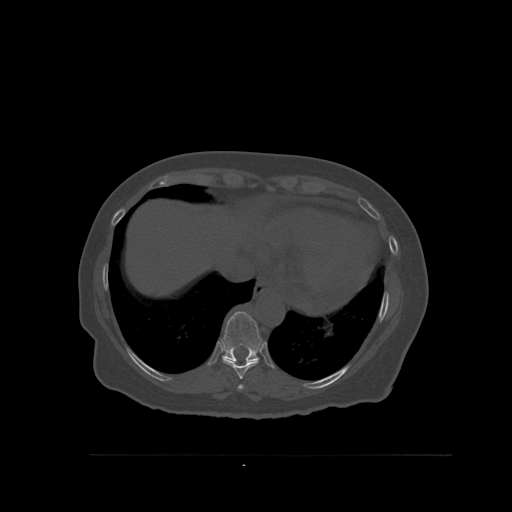
CT including the spine, one axial slice; position 328 of 527 along the scan axis; bone window (W 1800 / L 400 HU); 1.5 mm slice thickness; 512 × 512 image matrix, field of view 470 × 470 mm. Patient: female, 73 years. Case-level facts recorded for this patient, not image findings: primary cancer: breast; vertebrae with lytic lesions (as recorded): L2.
Outlined on this slice (semi-automatic segmentation, software-assisted and operator-edited):
- T10 vertebra: bounding box (x1, y1, x2, y2) in pixels: (221, 311, 262, 362)
- T8 vertebra: (237, 385, 244, 391)
- T9 vertebra: (222, 344, 259, 380)